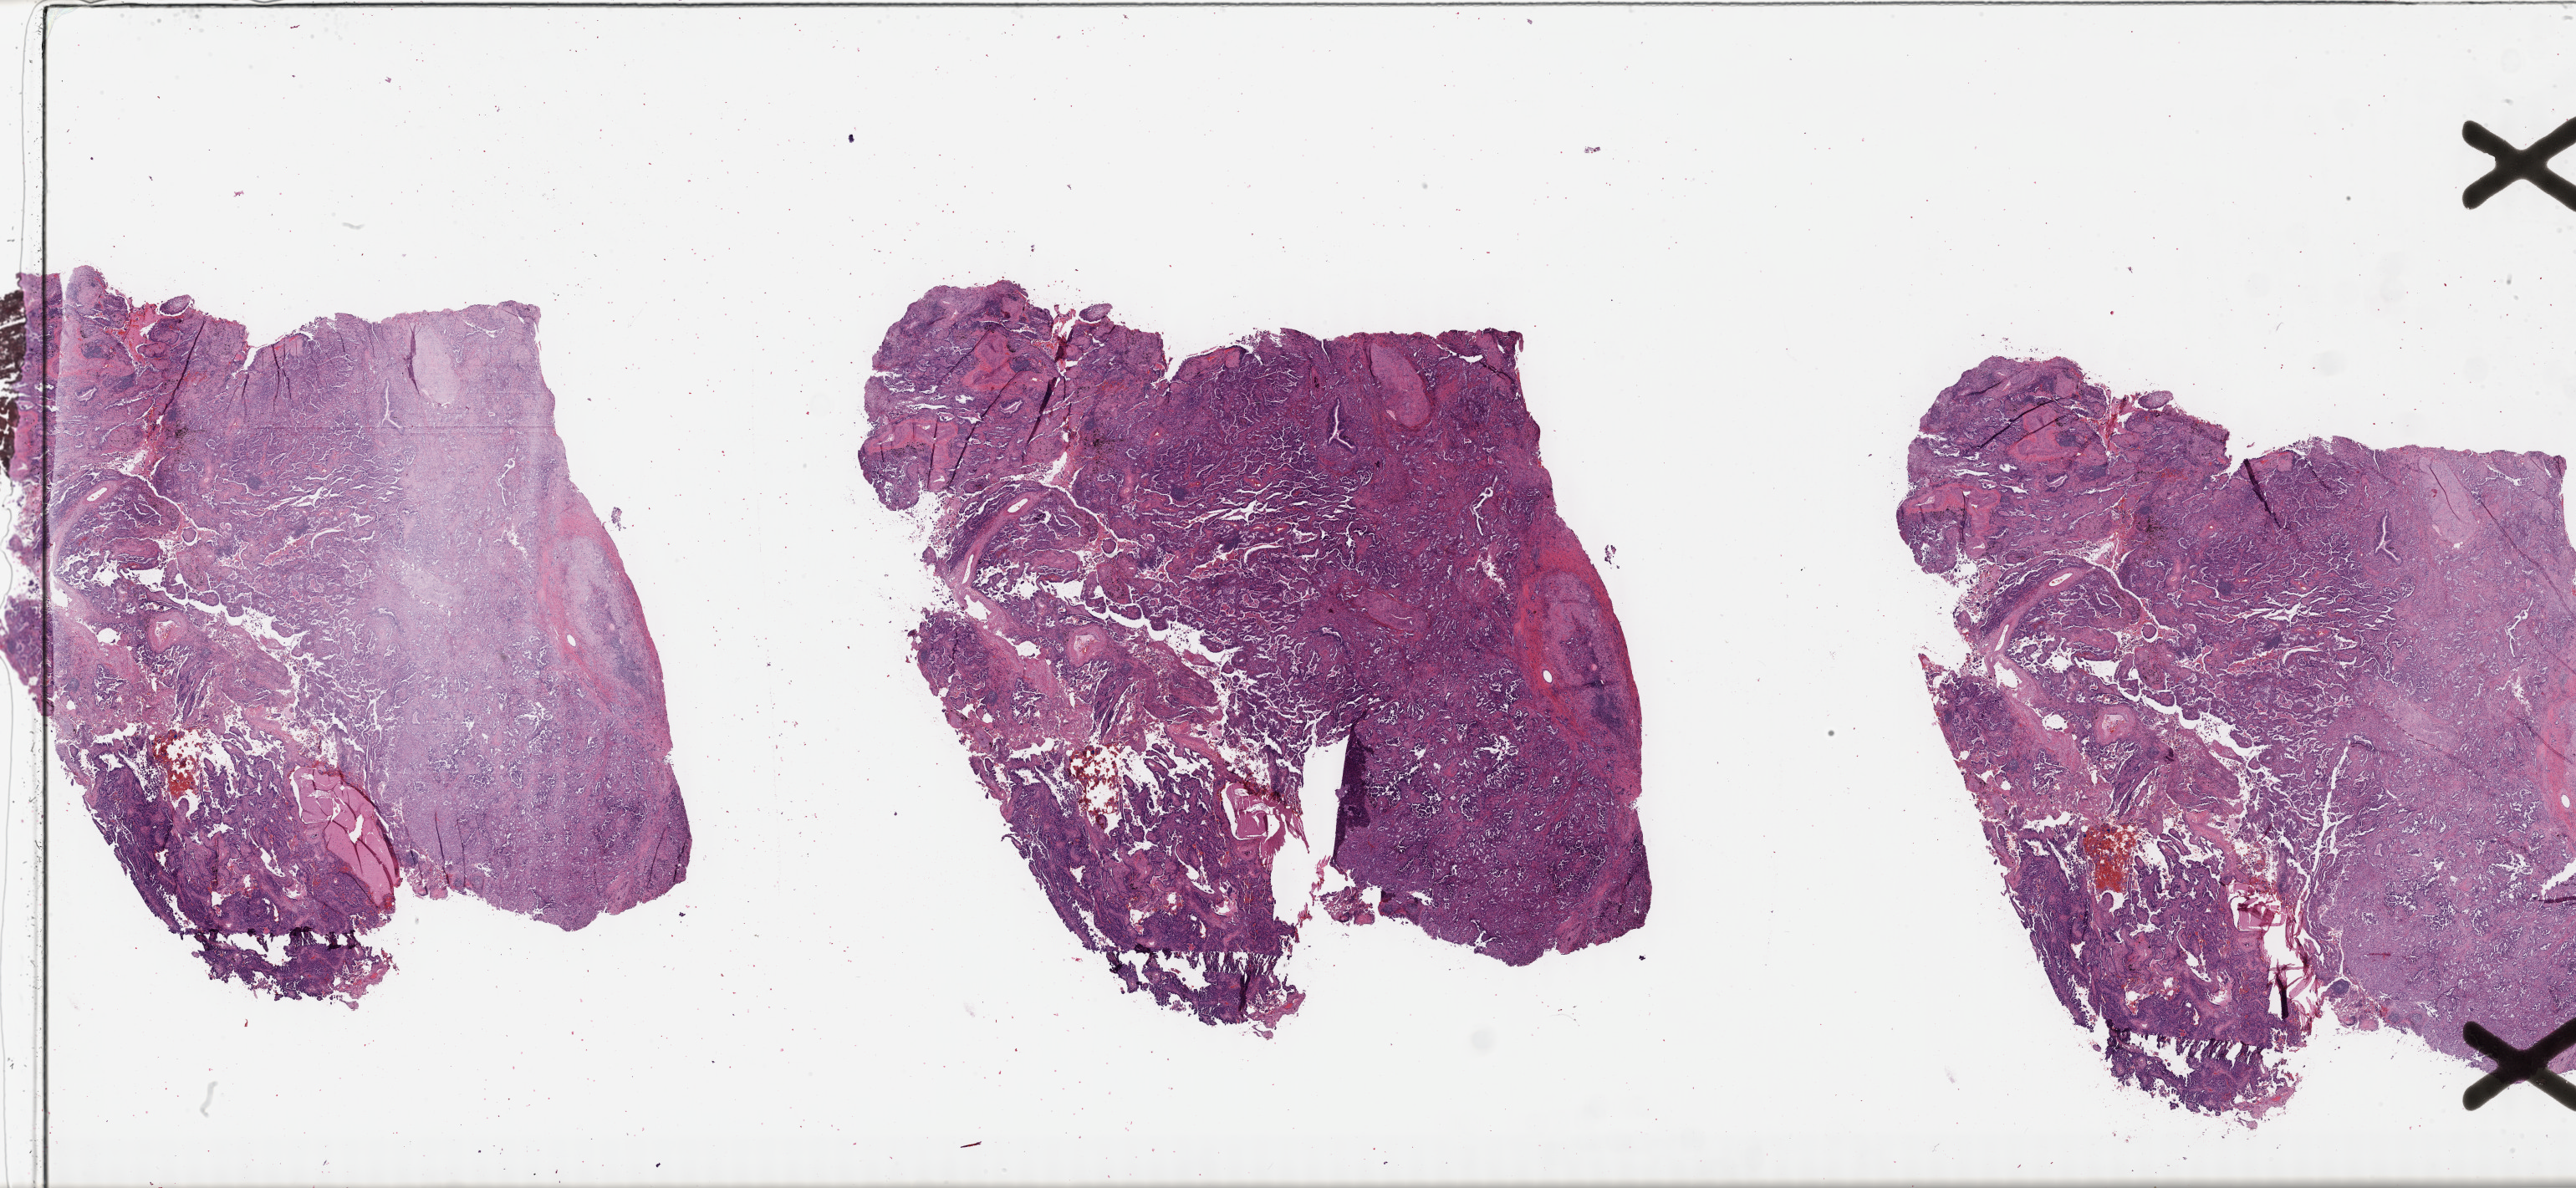
Digitized H&E tissue section (whole slide) — whole scanned area (about 49.8 x 23.0 mm, slide scanned at 40x) shown as a low-resolution overview. FFPE section. Sample: primary tumour, lung. Patient: female, age at initial diagnosis 87 years.
Diagnosis: Acinar cell carcinoma (upper lobe, lung).